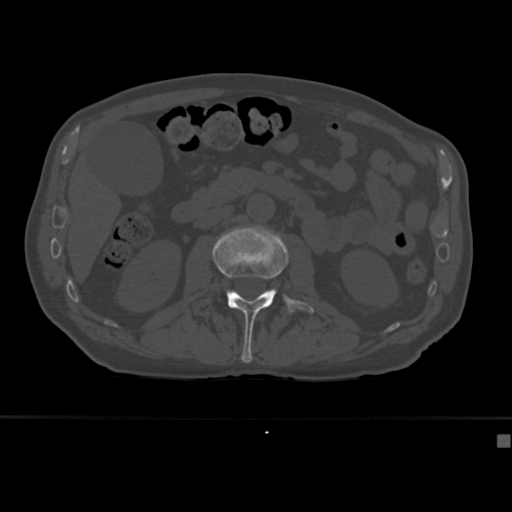
CT including the spine, one axial slice. 120 kVp. Bone window (W 1800 / L 400 HU). 1.5 mm slice thickness. 512 × 512 image matrix, field of view 337 × 337 mm. Male patient, age 64 years. From the clinical record (not read from this slice): primary cancer: uterus; vertebrae with lytic lesions (as recorded): T1, T4, T5, T7, L5.
Outlined on this slice (semi-automatically segmented with operator editing):
- L2 vertebra: bounding box [x1, y1, x2, y2] px = [212, 226, 315, 363]